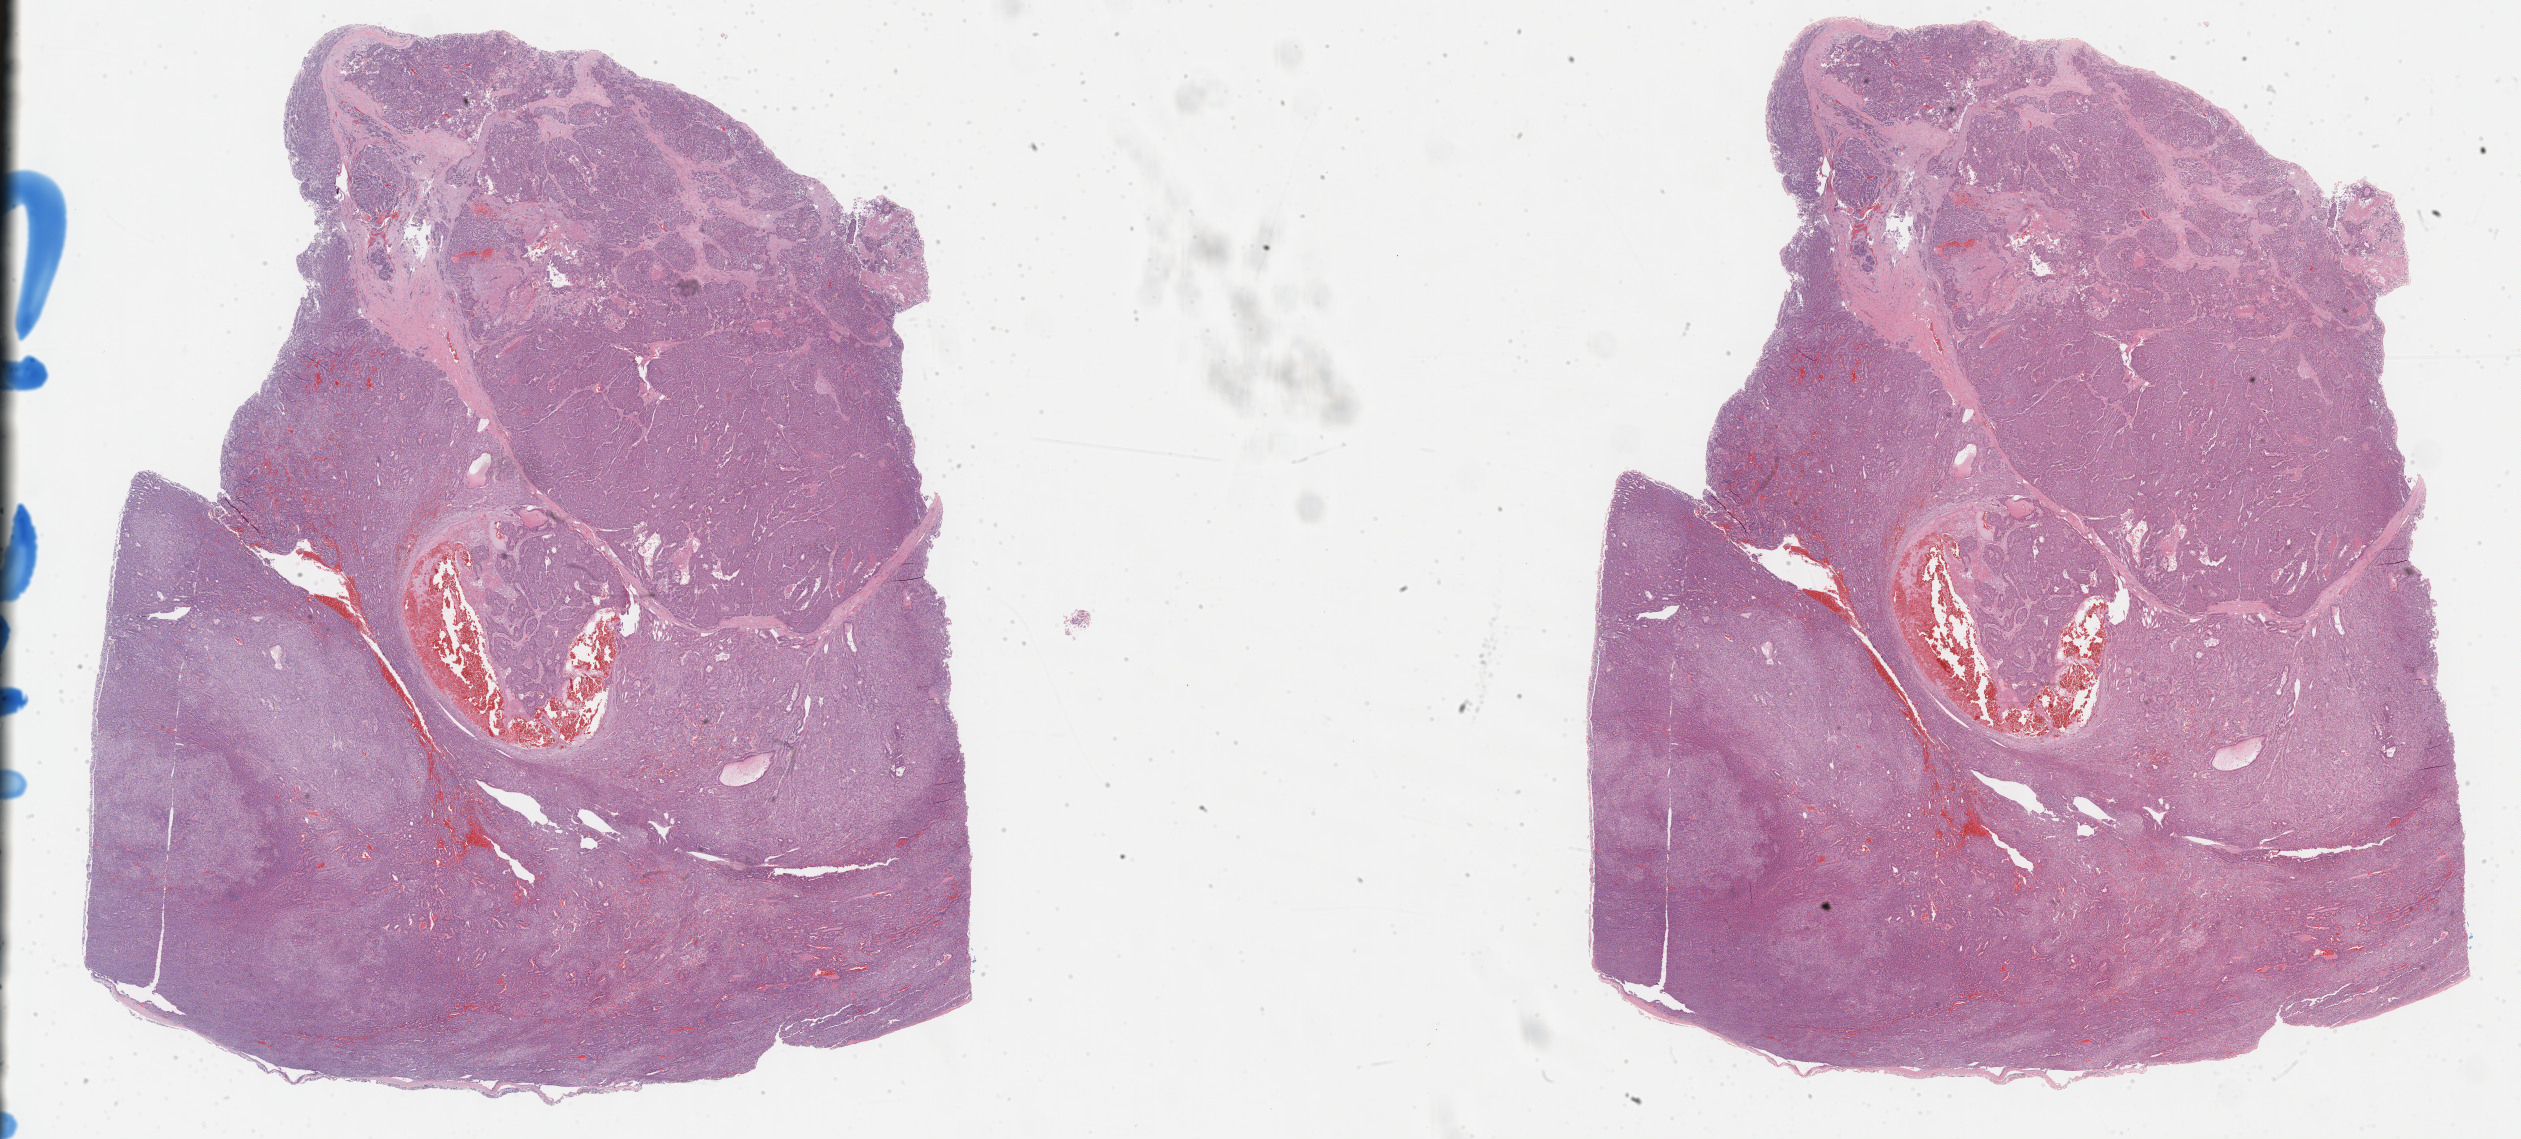
Digitized H&E-stained tissue section (whole slide), whole scanned area (about 40.8 x 18.4 mm) shown as a low-resolution overview. Formalin-fixed paraffin-embedded (FFPE) diagnostic section. Sample: primary tumour, adrenal cortex. Female, age 69 years at initial diagnosis.
- laterality: left
- histologic diagnosis: Adrenal cortical carcinoma (cortex of adrenal gland)